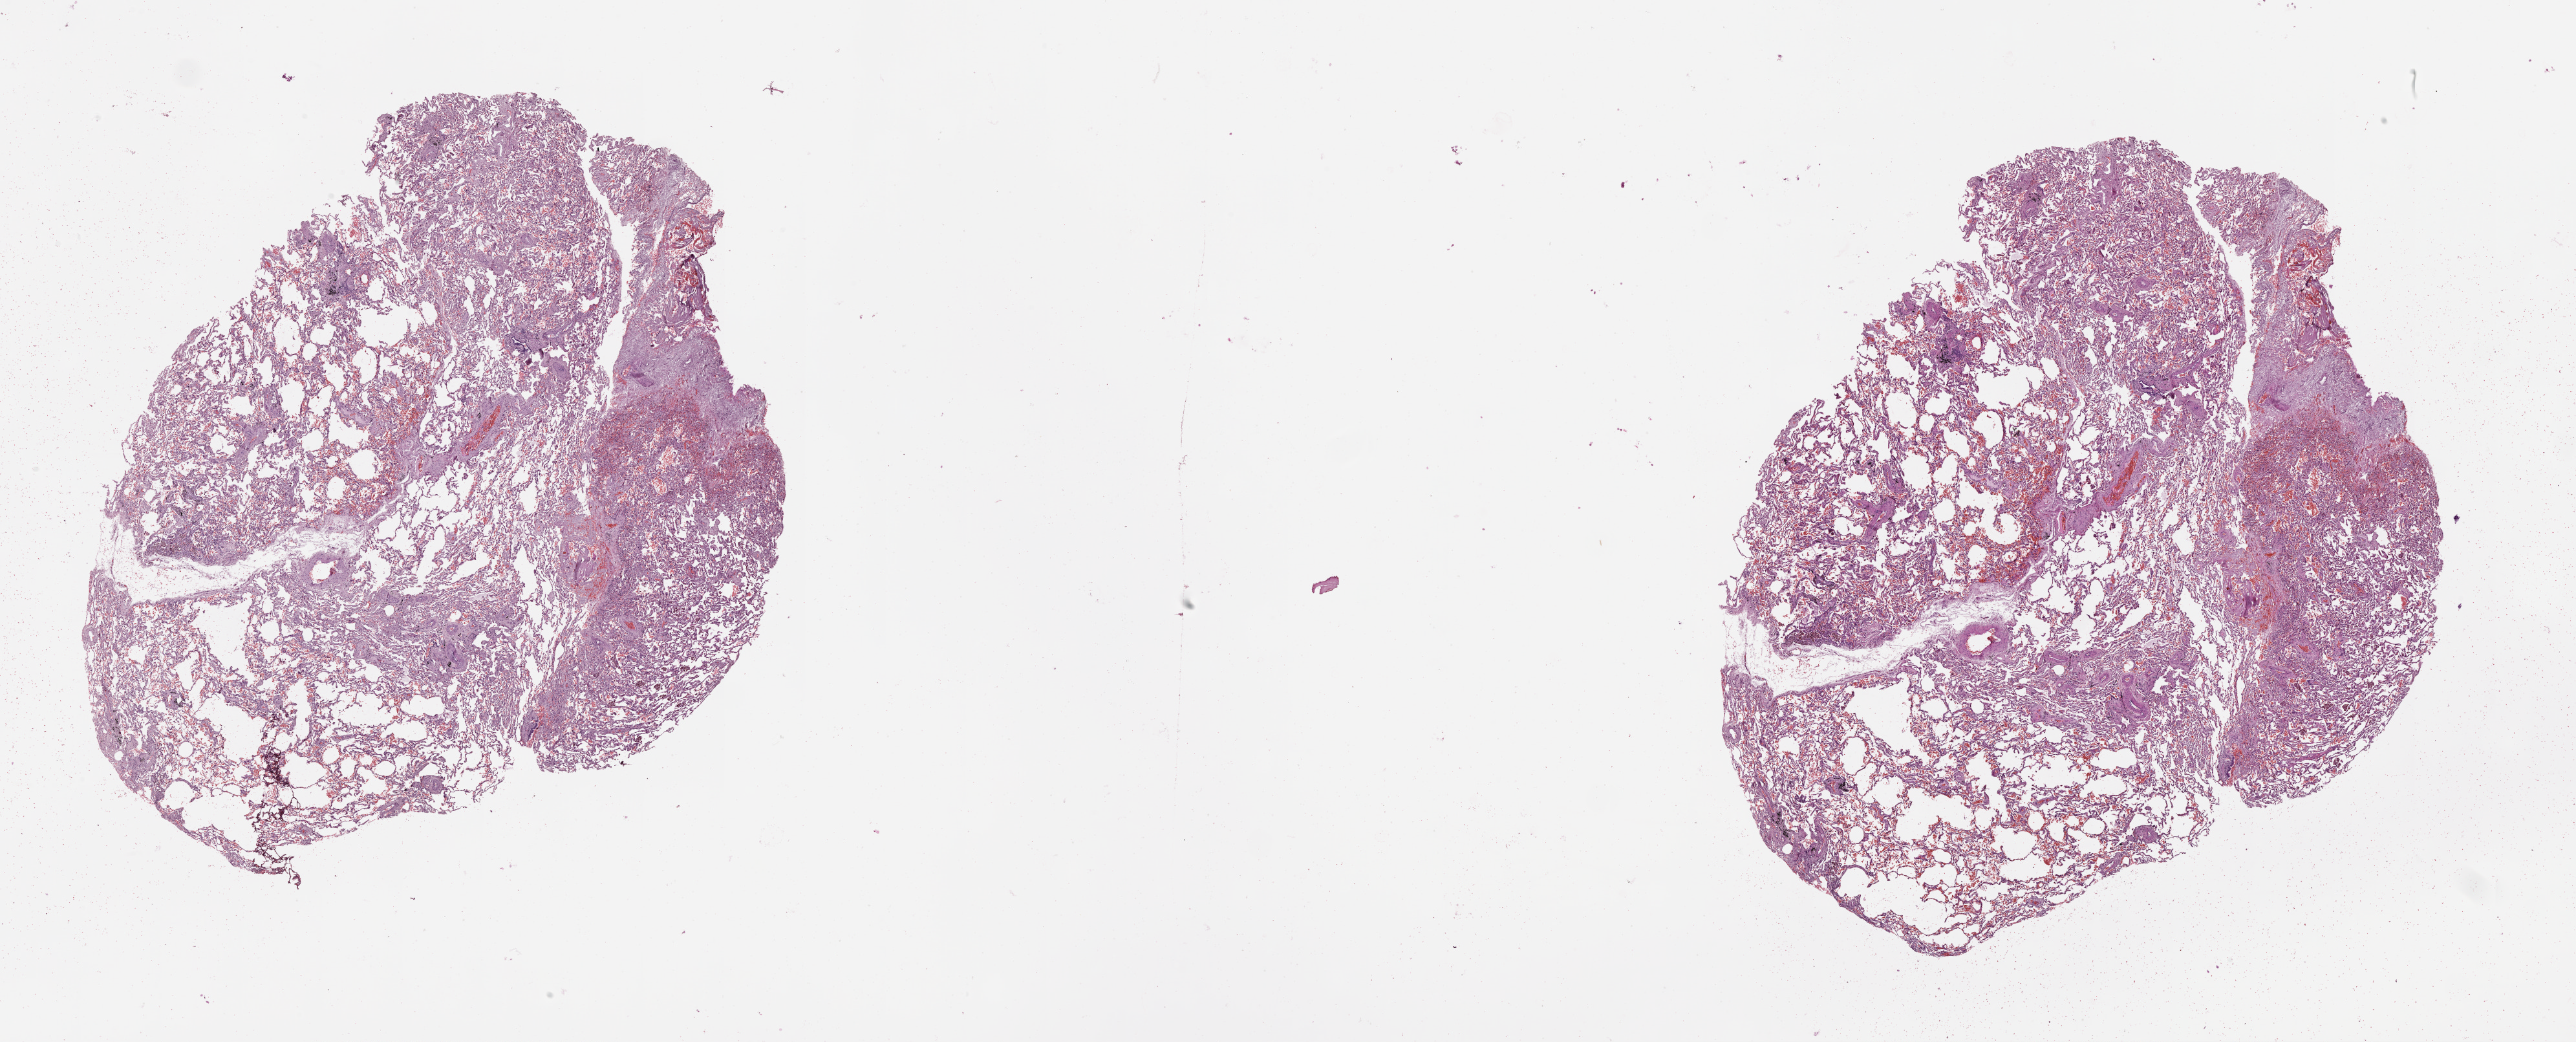
Digitized H&E-stained tissue section (whole slide) — whole scanned area (about 32.1 x 13.0 mm) shown as a low-resolution overview. Normal (non-tumour) tissue sample, lung. 63-year-old female patient.
• this section: normal (non-tumour) tissue from the same patient
• patient diagnosis (cohort enrolment): squamous cell carcinoma (lung)